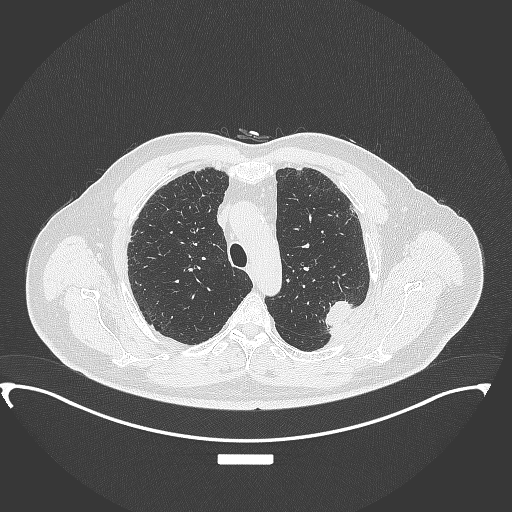
Chest CT, one axial slice. Slice 274 of 350 in the series (ordered by position). Lung window (W 1500 / L -600 HU). 512 × 512 image matrix. Patient: male, 64 years. From the clinical record (not read from this slice): clinical TNM (as recorded): T1c N1 M1.
Annotated regions visible in this slice (rectangle marked by the reading radiologist):
- lung tumour (recorded histology: adenocarcinoma): box from (x=320, y=298) to (x=359, y=334) px